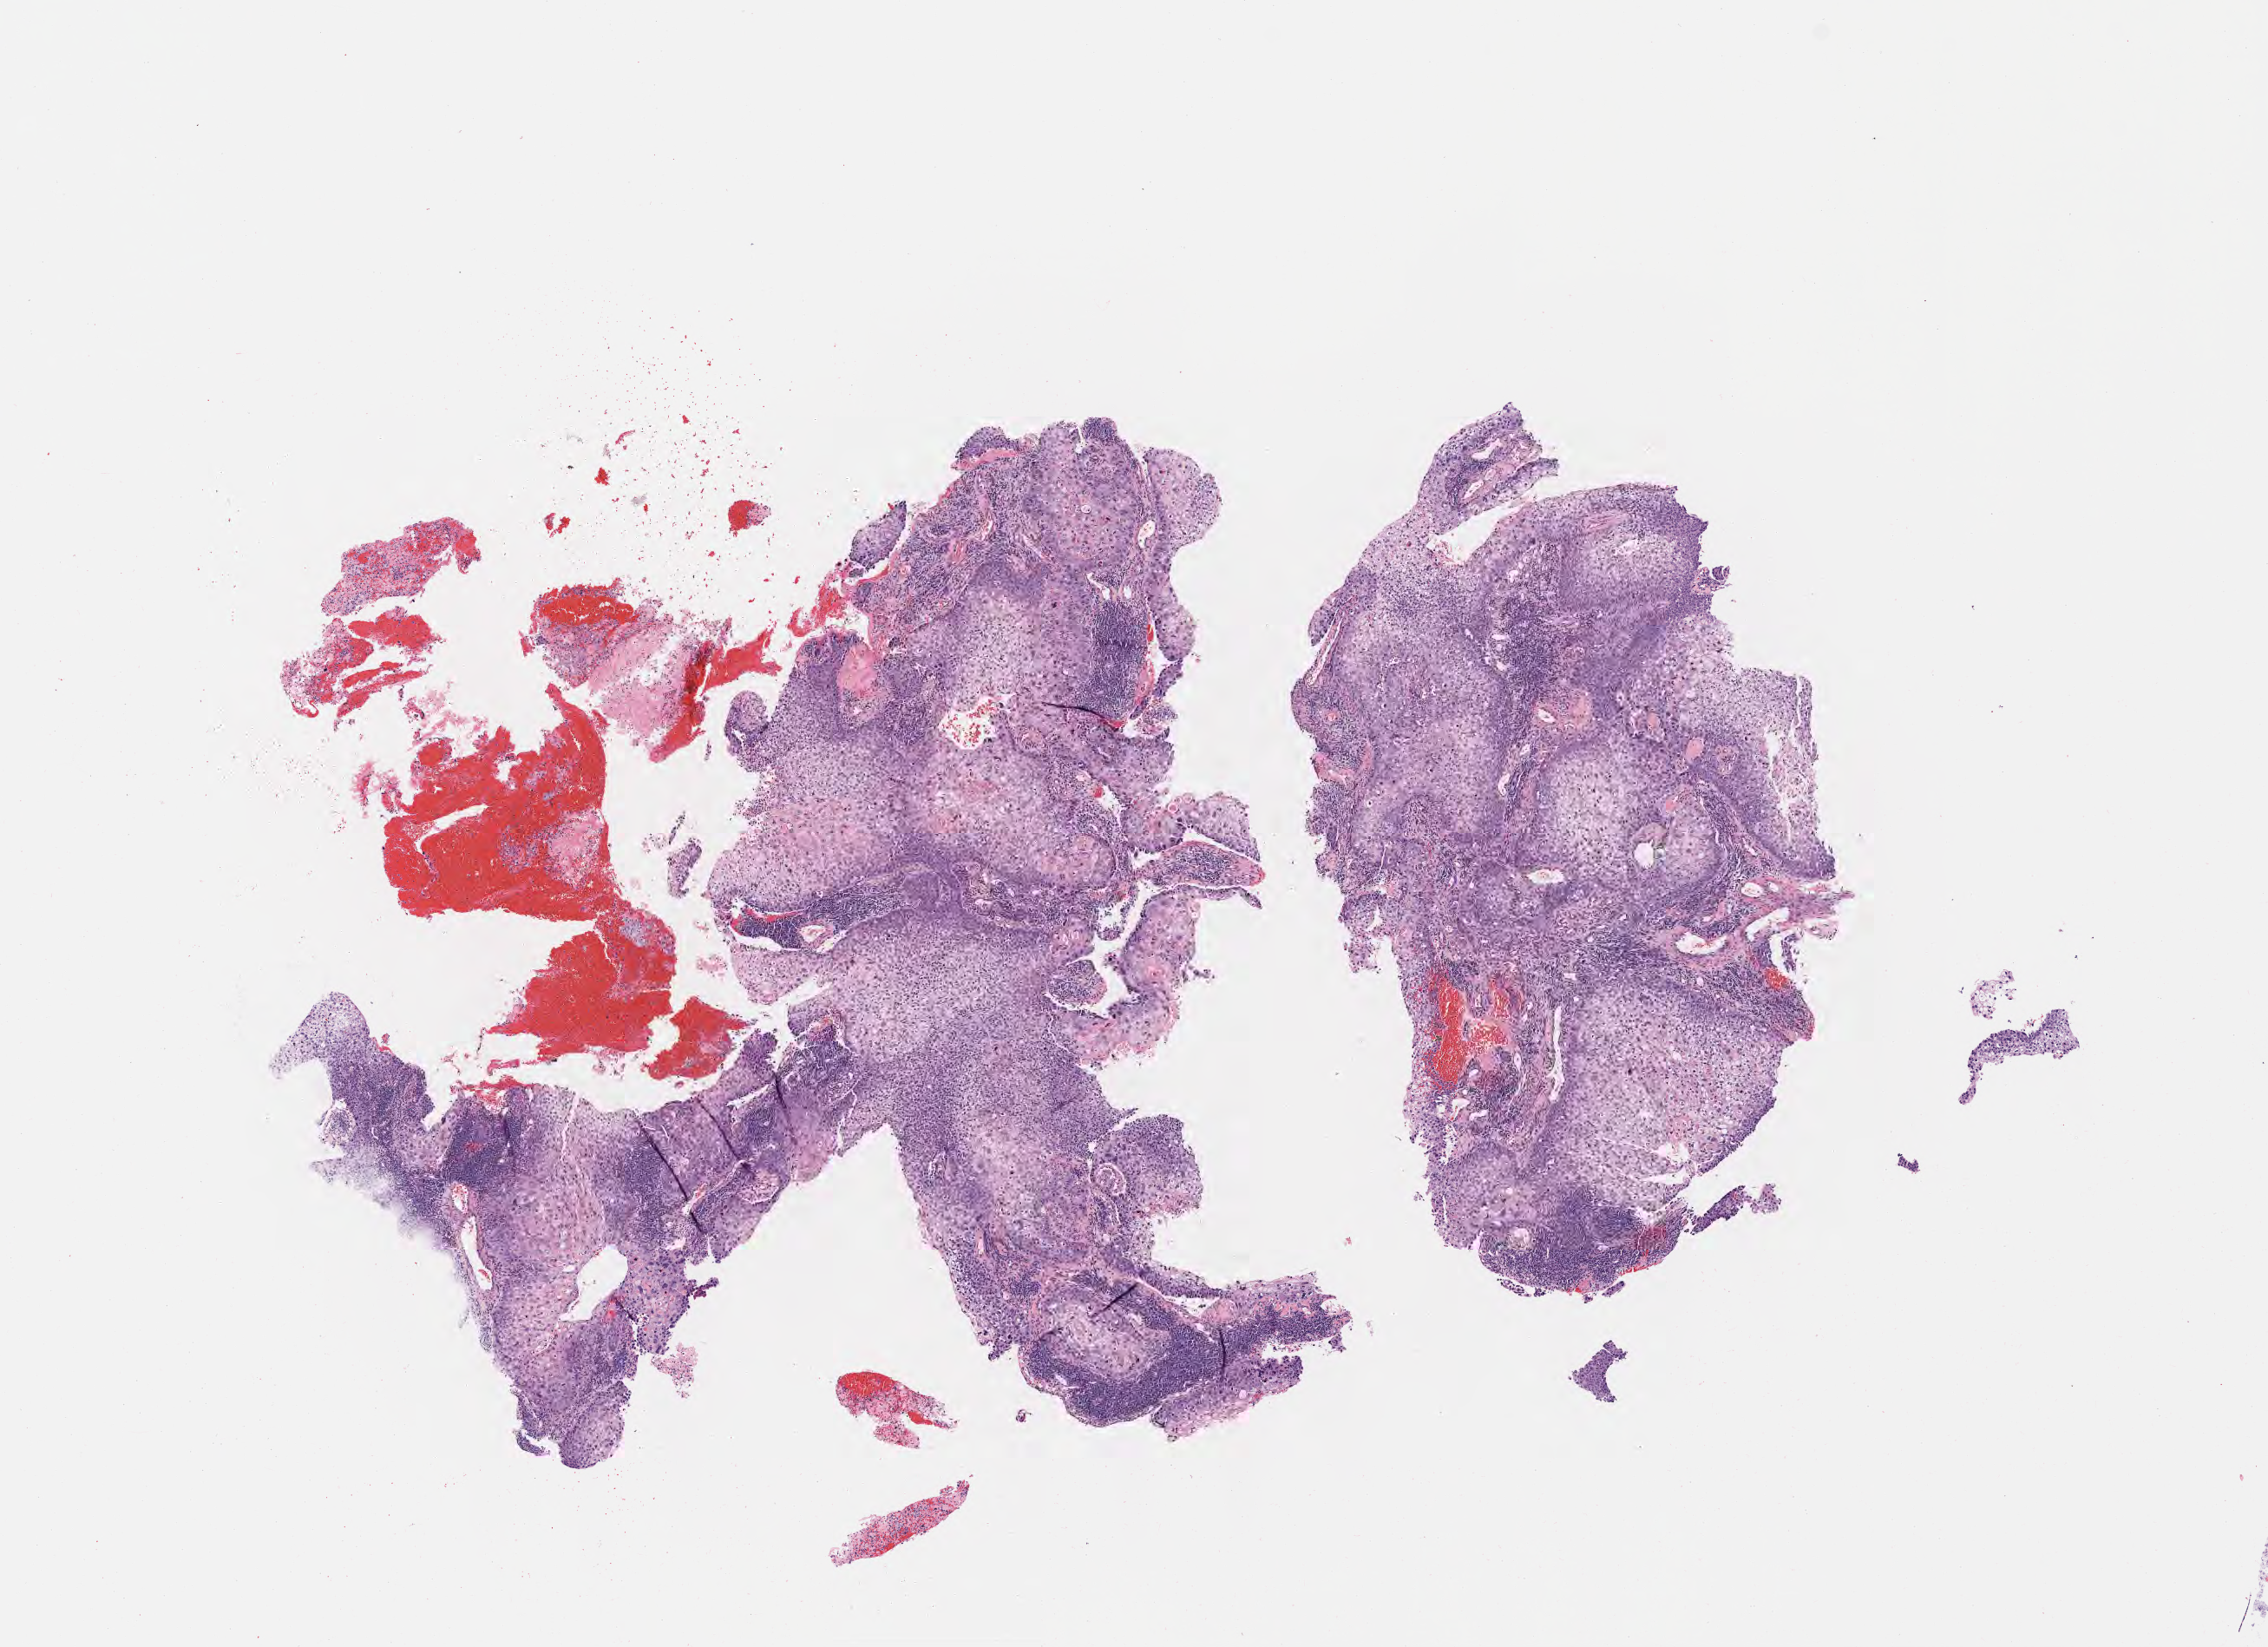
Digitized haematoxylin and eosin-stained section — low-resolution overview of the scanned area, about 10.6 x 7.7 mm; tumor tissue; site: cervix. Patient: female, 43 years old.
Histologic diagnosis: Squamous cell carcinoma, keratinizing, NOS.